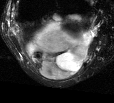
MRI of an extremity soft-tissue mass, one axial slice. Slice 19 of 44 in the series (ordered by position). T2-weighted fat-saturated. MR volume resampled by the dataset authors to the PET/CT grid (not the native acquisition matrix). 114 × 103 image matrix, field of view 111 × 101 mm. Female patient. From the clinical record (not read from this slice): histological type: liposarcoma; site of the primary tumour: right thigh.
Annotated regions visible in this slice (expert contour drawn on MRI and transferred to this co-registered scan by the dataset authors):
- gross tumour volume (mass): bounding box <25,20,96,81> (left, top, right, bottom; pixels)